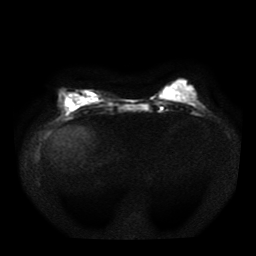
Breast MRI, one axial slice. Position 14 of 41 along the scan axis. Diffusion-weighted series; image 2 of 4 stored at this slice position (different b-values; order by instance number). 1.5 T. 5 mm slice thickness. 256 × 256 image matrix, field of view 330 × 330 mm. Female patient.
Annotated regions visible in this slice (expert manual segmentation):
- tumour on diffusion-weighted imaging: bounding box [x1, y1, x2, y2] px = [67, 102, 74, 111]